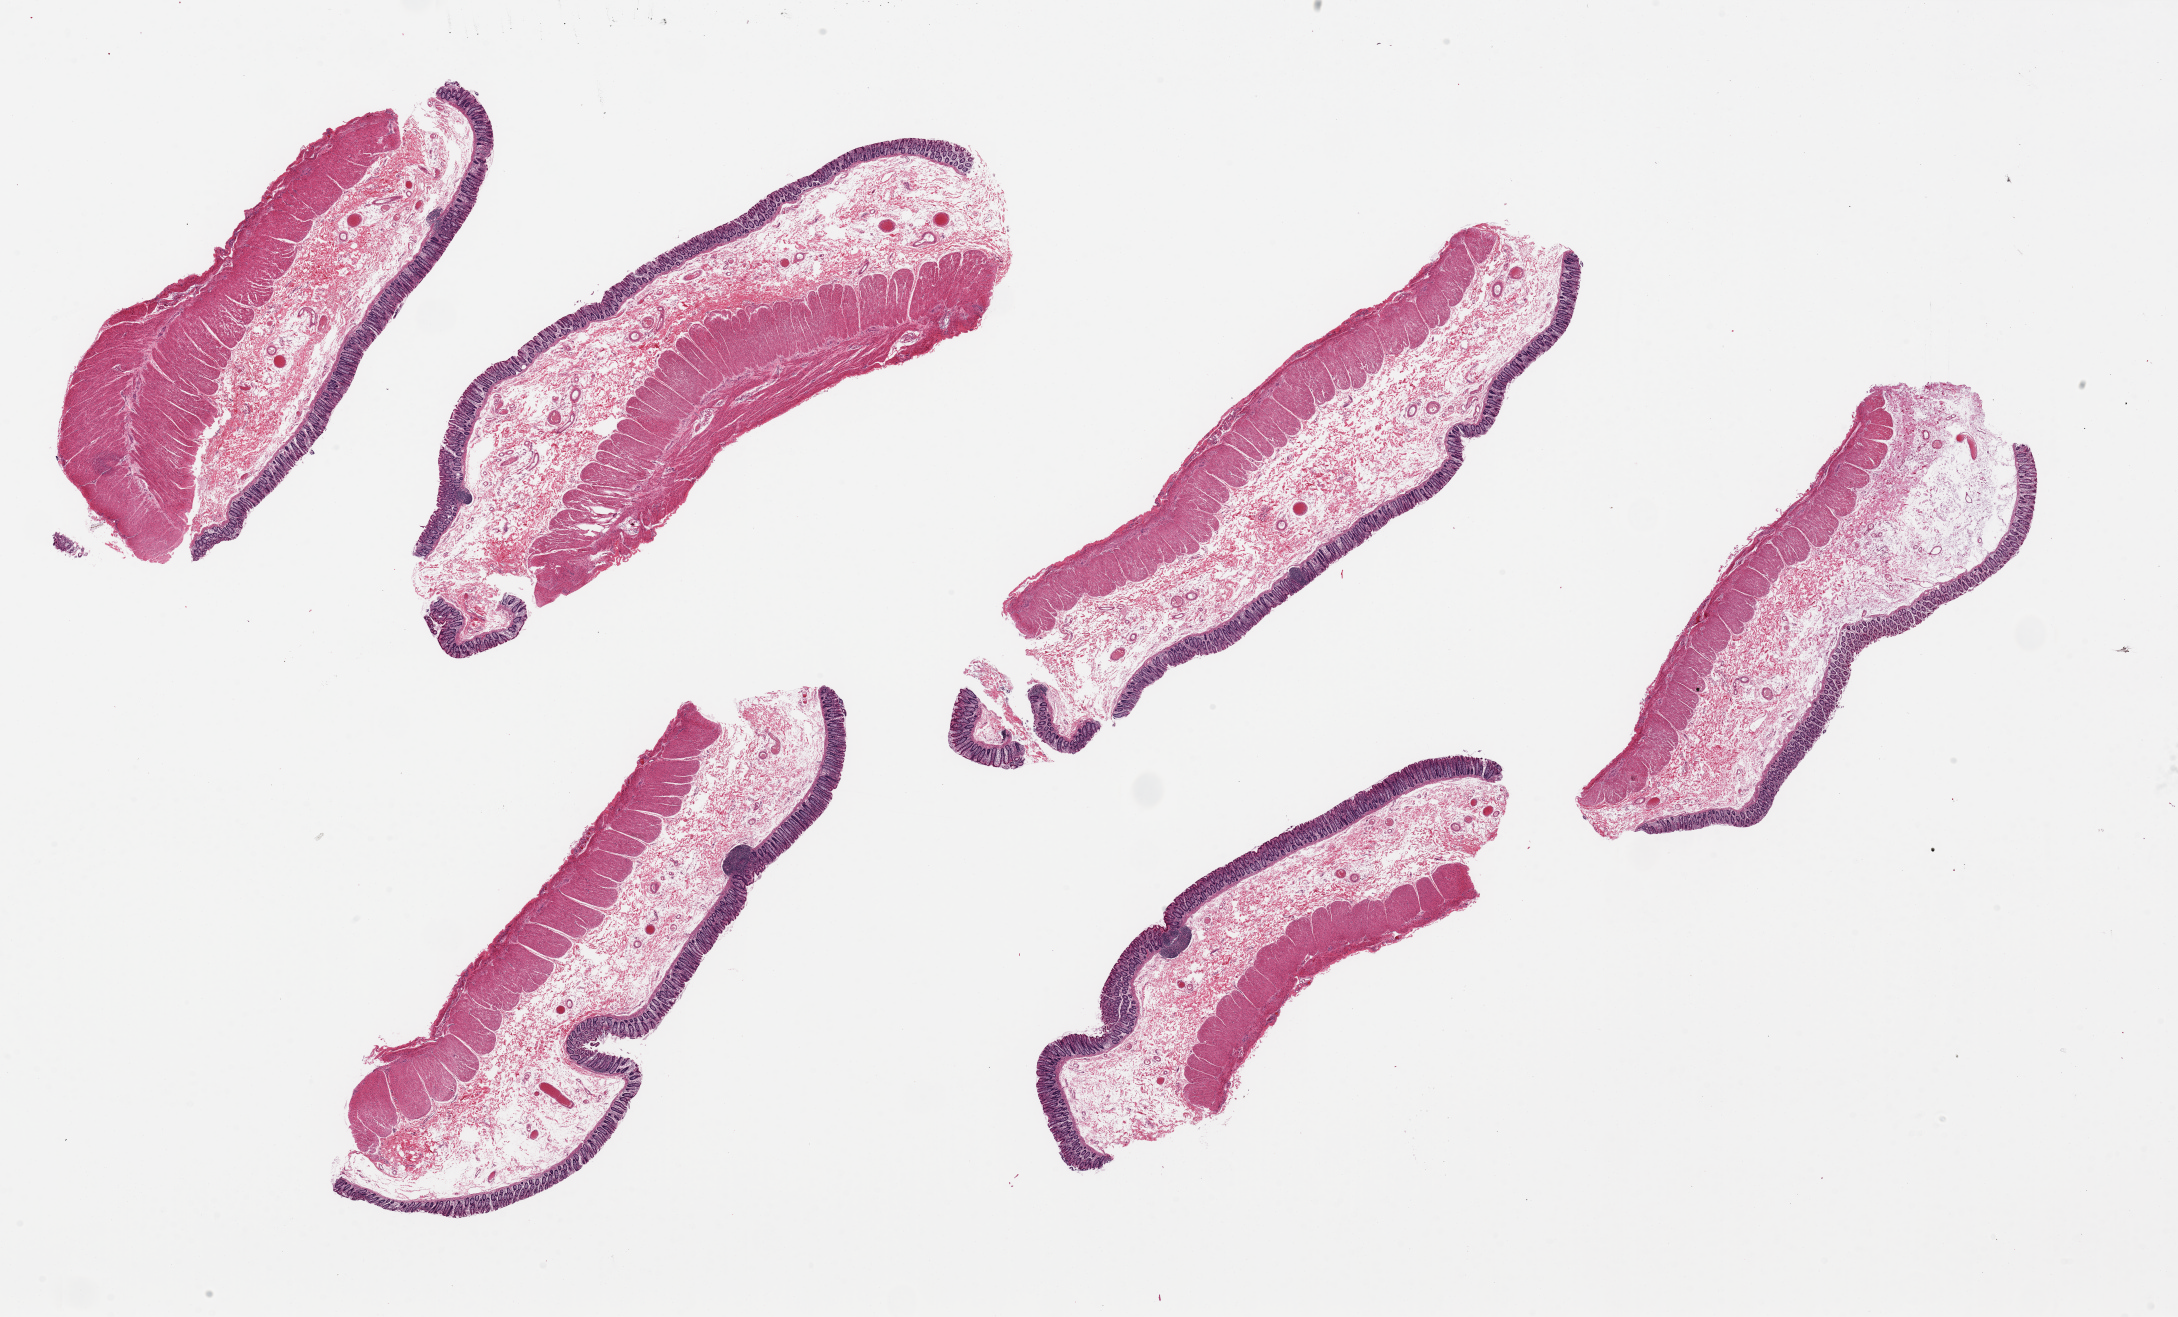
Digitized hematoxylin and eosin (H&E)-stained section — low-resolution overview of the scanned area, about 34.5 x 20.8 mm; PAXgene-fixed, paraffin-embedded tissue; target tissue: transverse colon; tissue donor sample. Donor: male.
Review note (as recorded): 6 pieces, ~9x3mm. Mucosa reasonably well-preserved, ~10% of thickness.